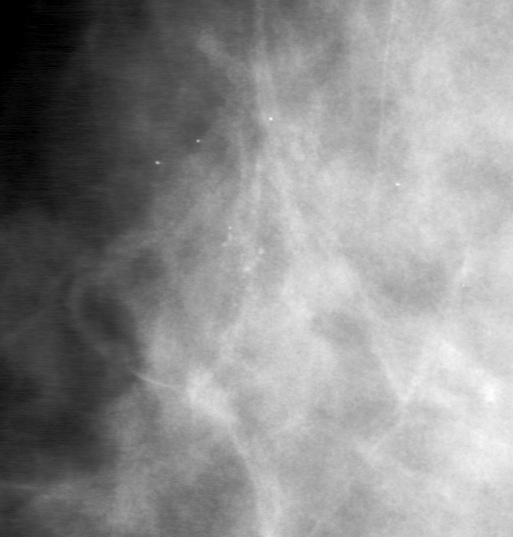
Region of interest cut from a scanned film mammogram (one marked finding), right breast, CC view, BI-RADS breast density category 3 (scale 1–4).
Calcifications, morphology punctate, distribution clustered; BI-RADS assessment category 0 (incomplete: needs additional imaging); pathology (as recorded): benign.